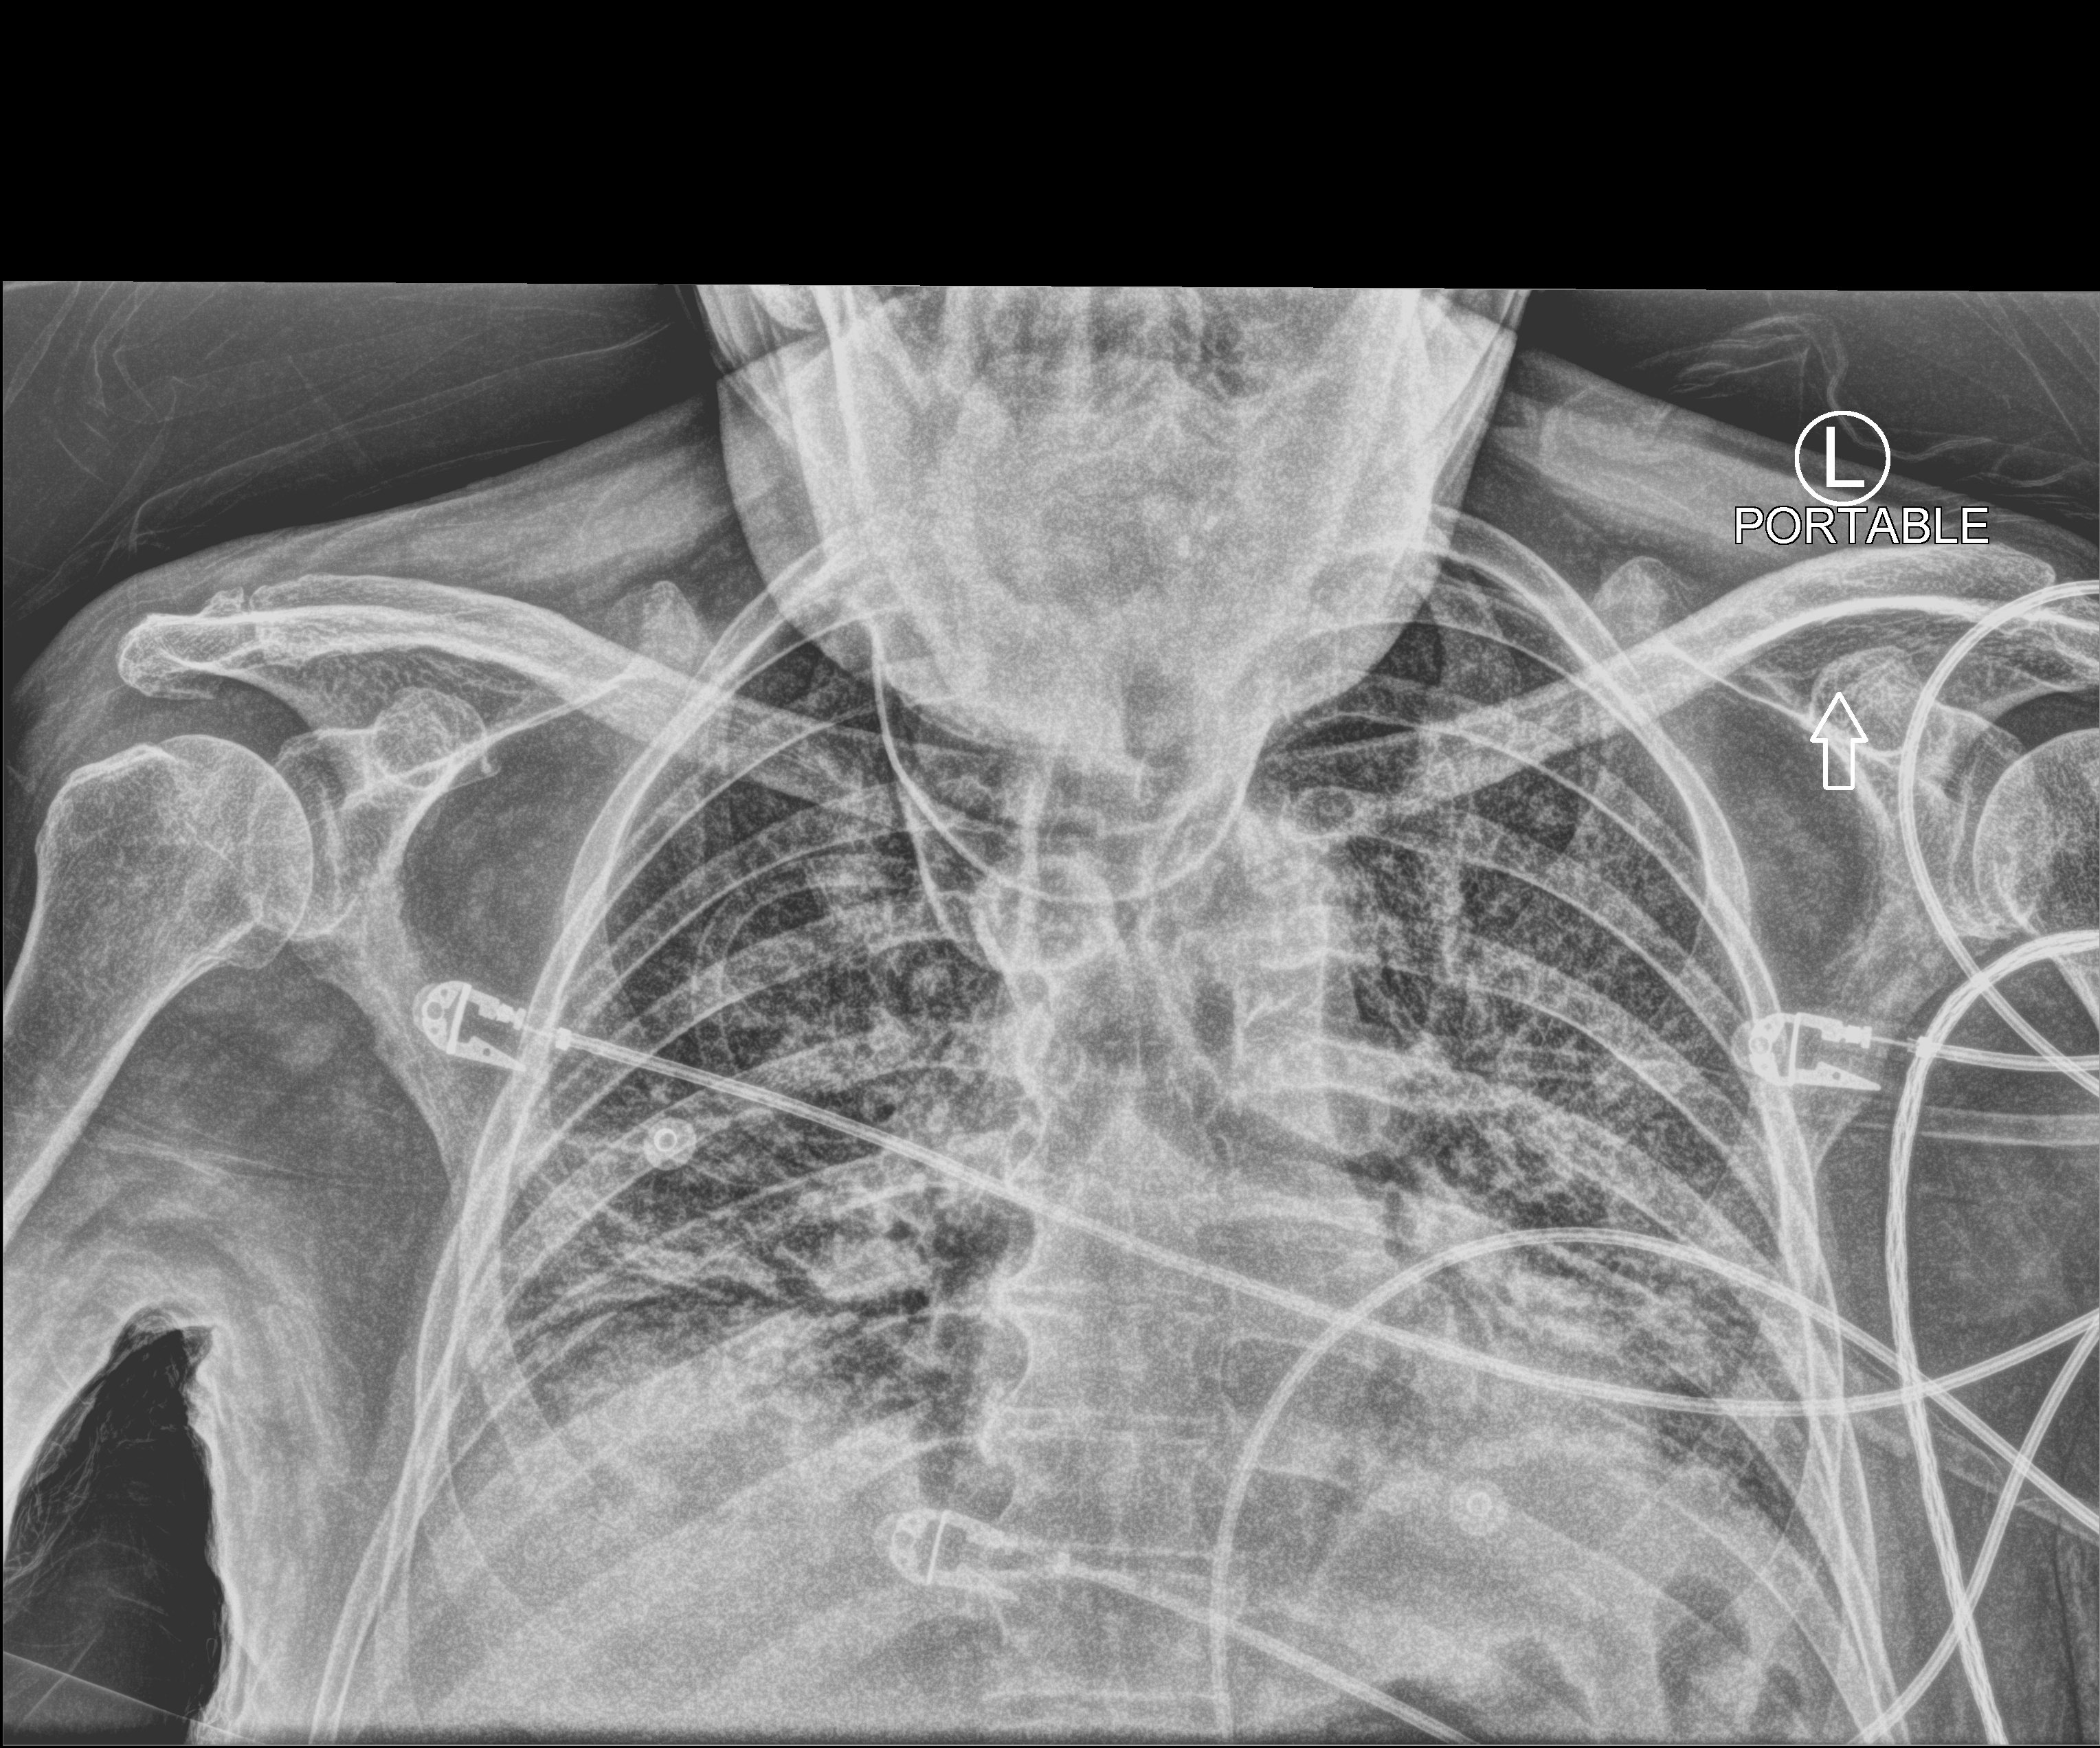
Chest X-ray (portable), anteroposterior (AP) projection. Male patient hospitalised with COVID-19, age 75–90 years.
From the hospital-stay record, not from the radiograph (when in the stay this image was taken is not recorded): chronic kidney disease (admission record): no.